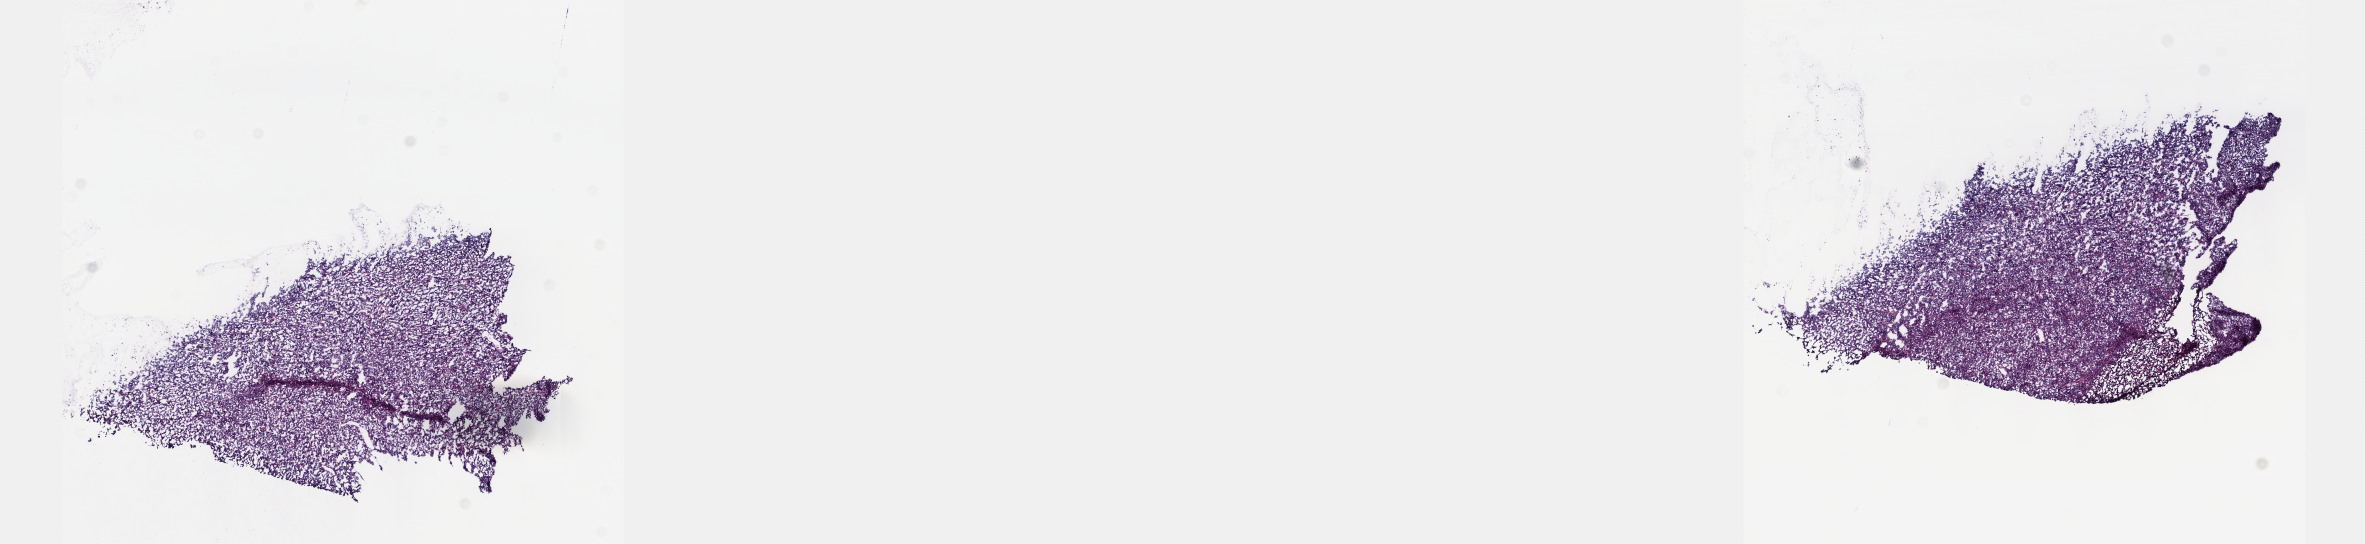
Digitized H&E tissue section (whole slide) — whole scanned area (about 19.1 x 4.4 mm, from a 40x scan) shown as a low-resolution overview. Frozen section from the top of the tissue portion. Uterus, primary tumour sample. Patient: female, age at initial diagnosis 56 years. Composition of this section per pathologist review: tumour cells 100%, tumour nuclei 80%, normal cells 0%, stromal cells 0%, necrosis 0%. Infiltration values recorded for this section: lymphocyte infiltration 1%, monocyte infiltration 0%, neutrophil infiltration 0%.
* histologic diagnosis: Leiomyosarcoma, NOS